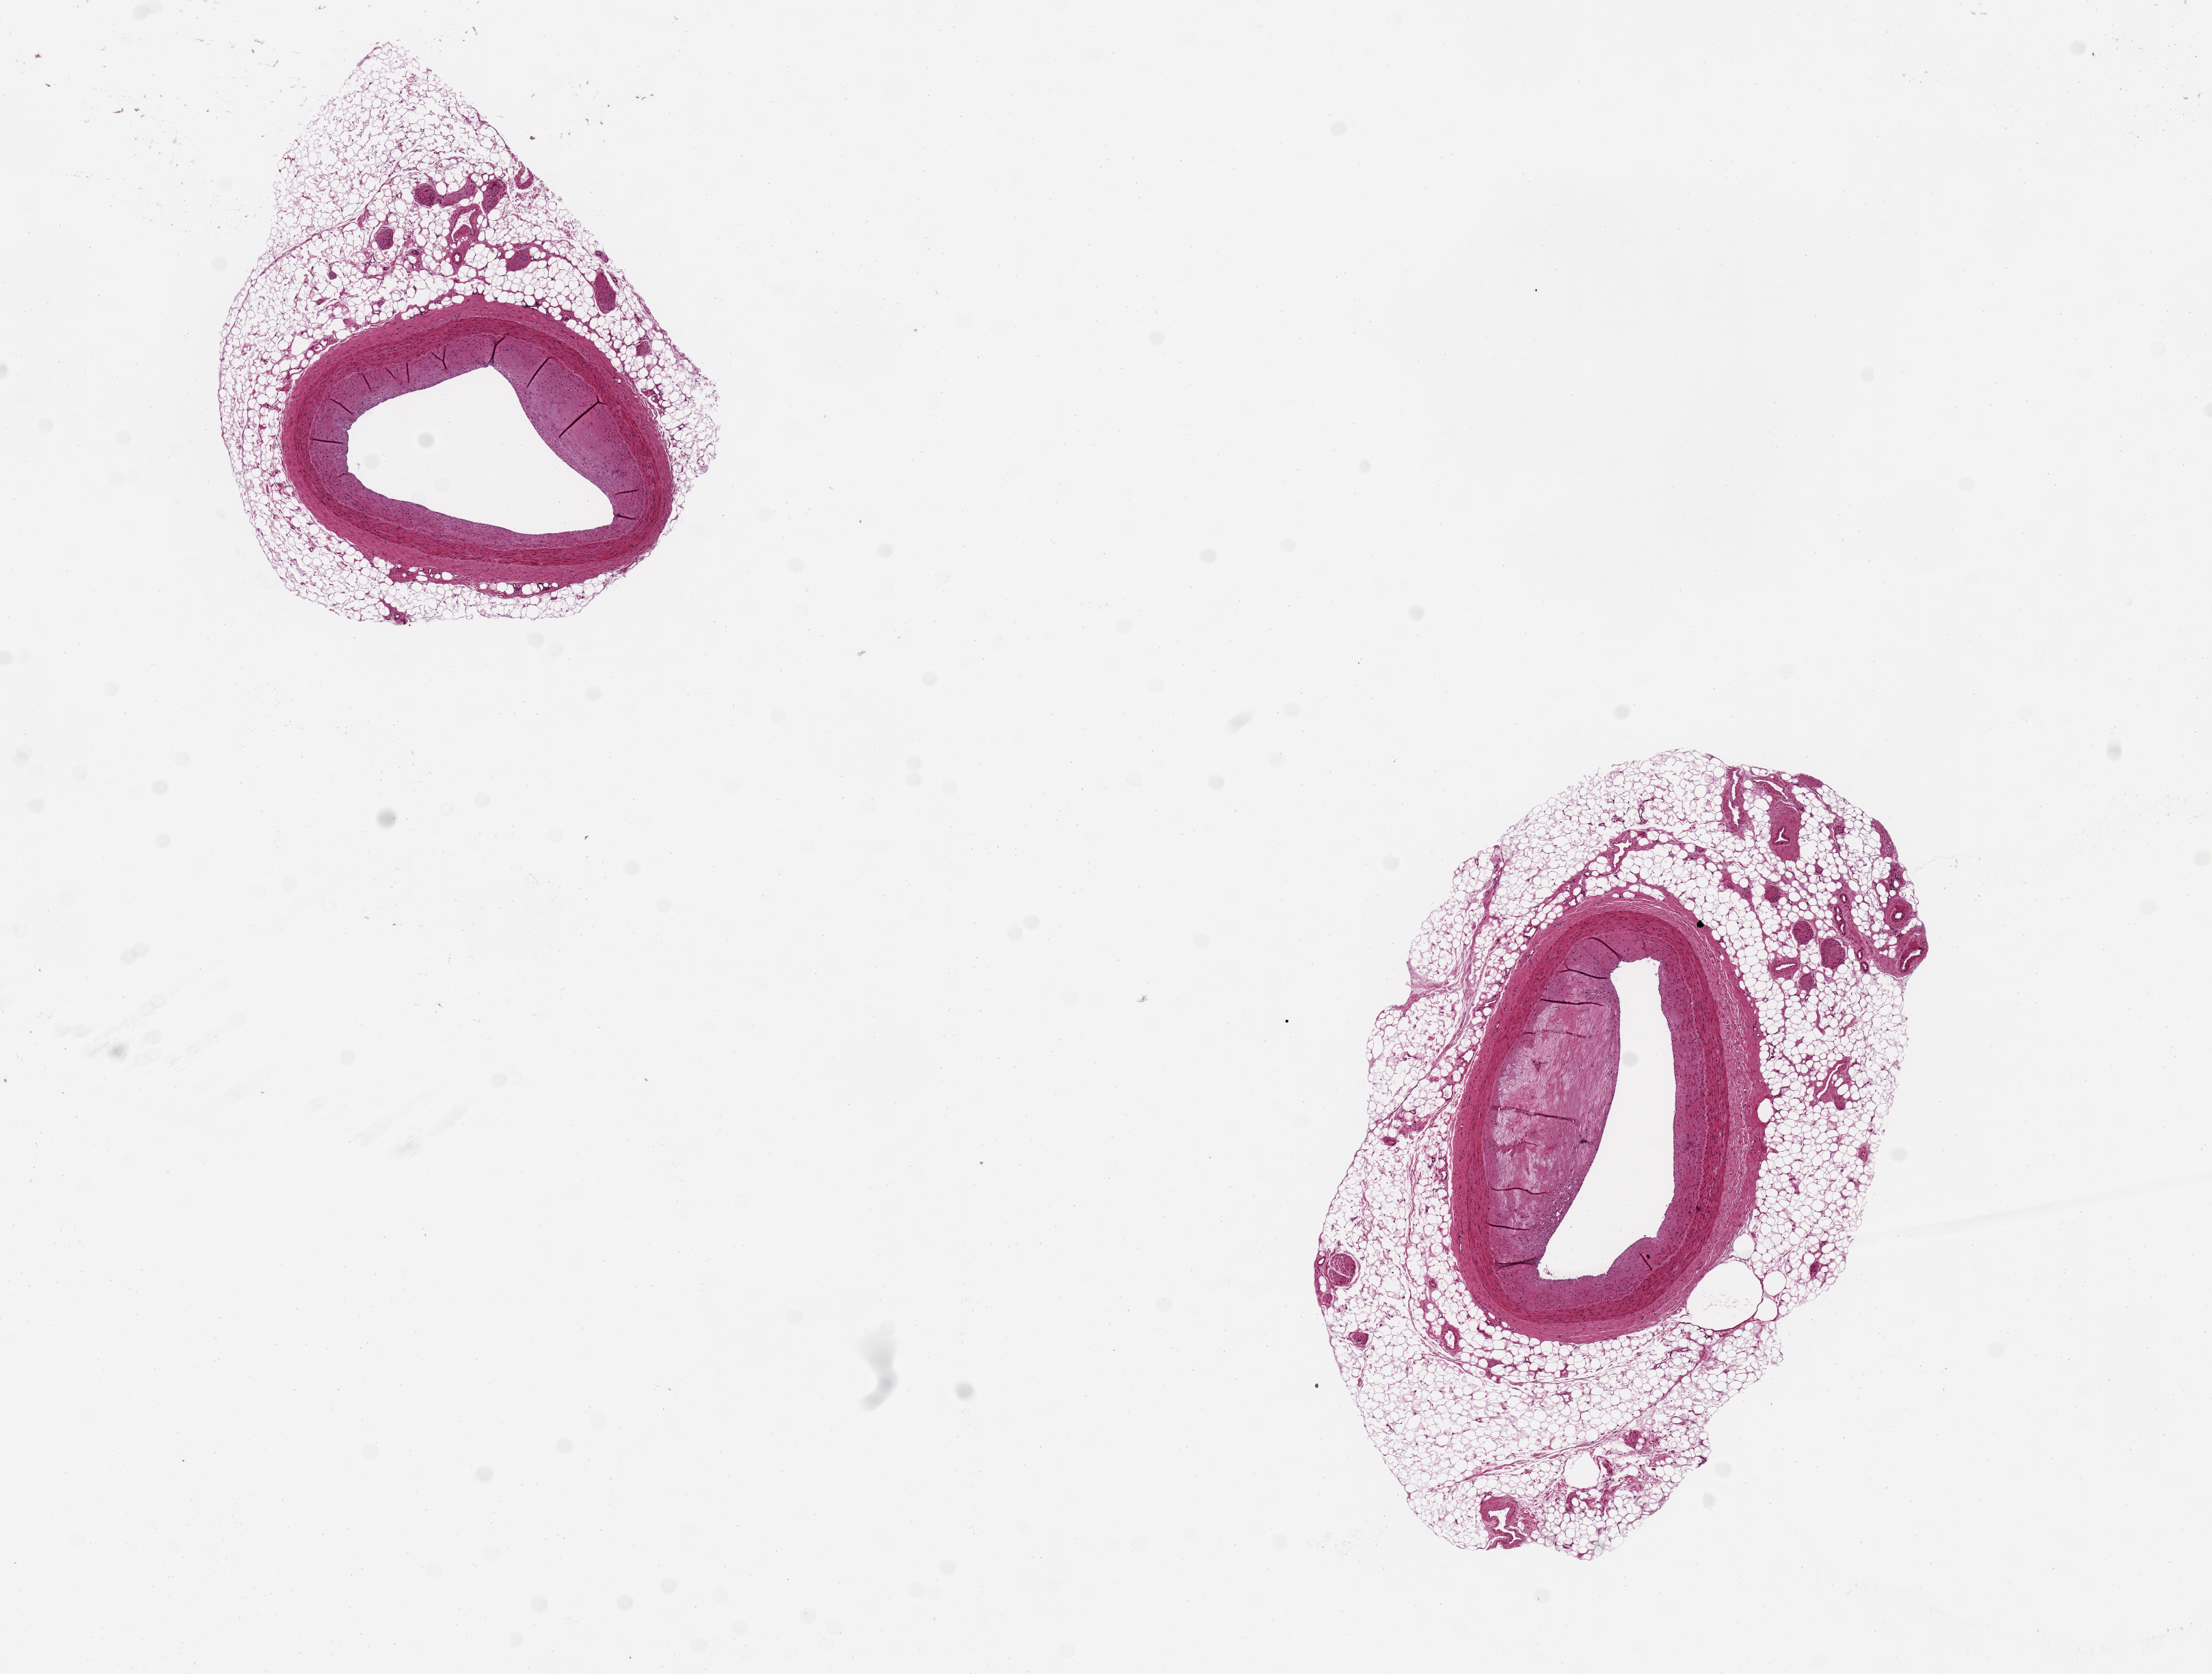
Digitized hematoxylin and eosin (H&E)-stained section, low-resolution overview of the scanned area, about 12.8 x 9.7 mm. PAXgene-fixed paraffin-embedded (PFPE) section. Target tissue: coronary artery. Donor tissue sample. Donor sex: male.
* pathologist's review note for this sample: 2 pieces, 3x2 & 2.8x2.5 mm; eccentric atheromatous plaque; both arteries encased in up to 1 mm adipose